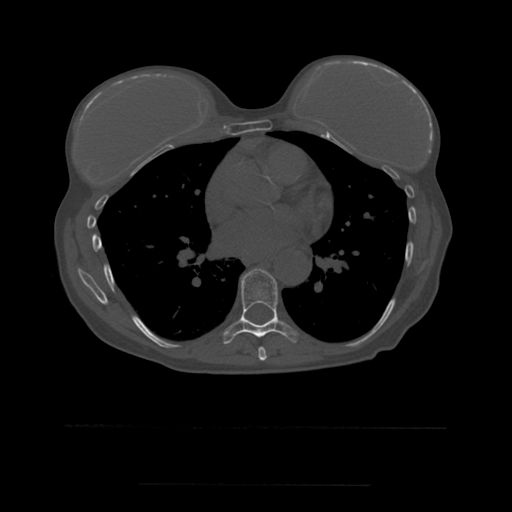
CT including the spine, one axial slice; slice 342 of 544 in the series (ordered by position); bone window (W 1800 / L 400 HU); 512 × 512 image matrix, field of view 350 × 350 mm. Patient age 58 years. From the clinical record (not read from this slice): primary cancer: lung.
Annotated regions visible in this slice (semi-automatically segmented with operator editing):
- T7 vertebra: box from (x=258, y=347) to (x=267, y=361) px
- T8 vertebra: (x=222, y=269)–(x=299, y=344)